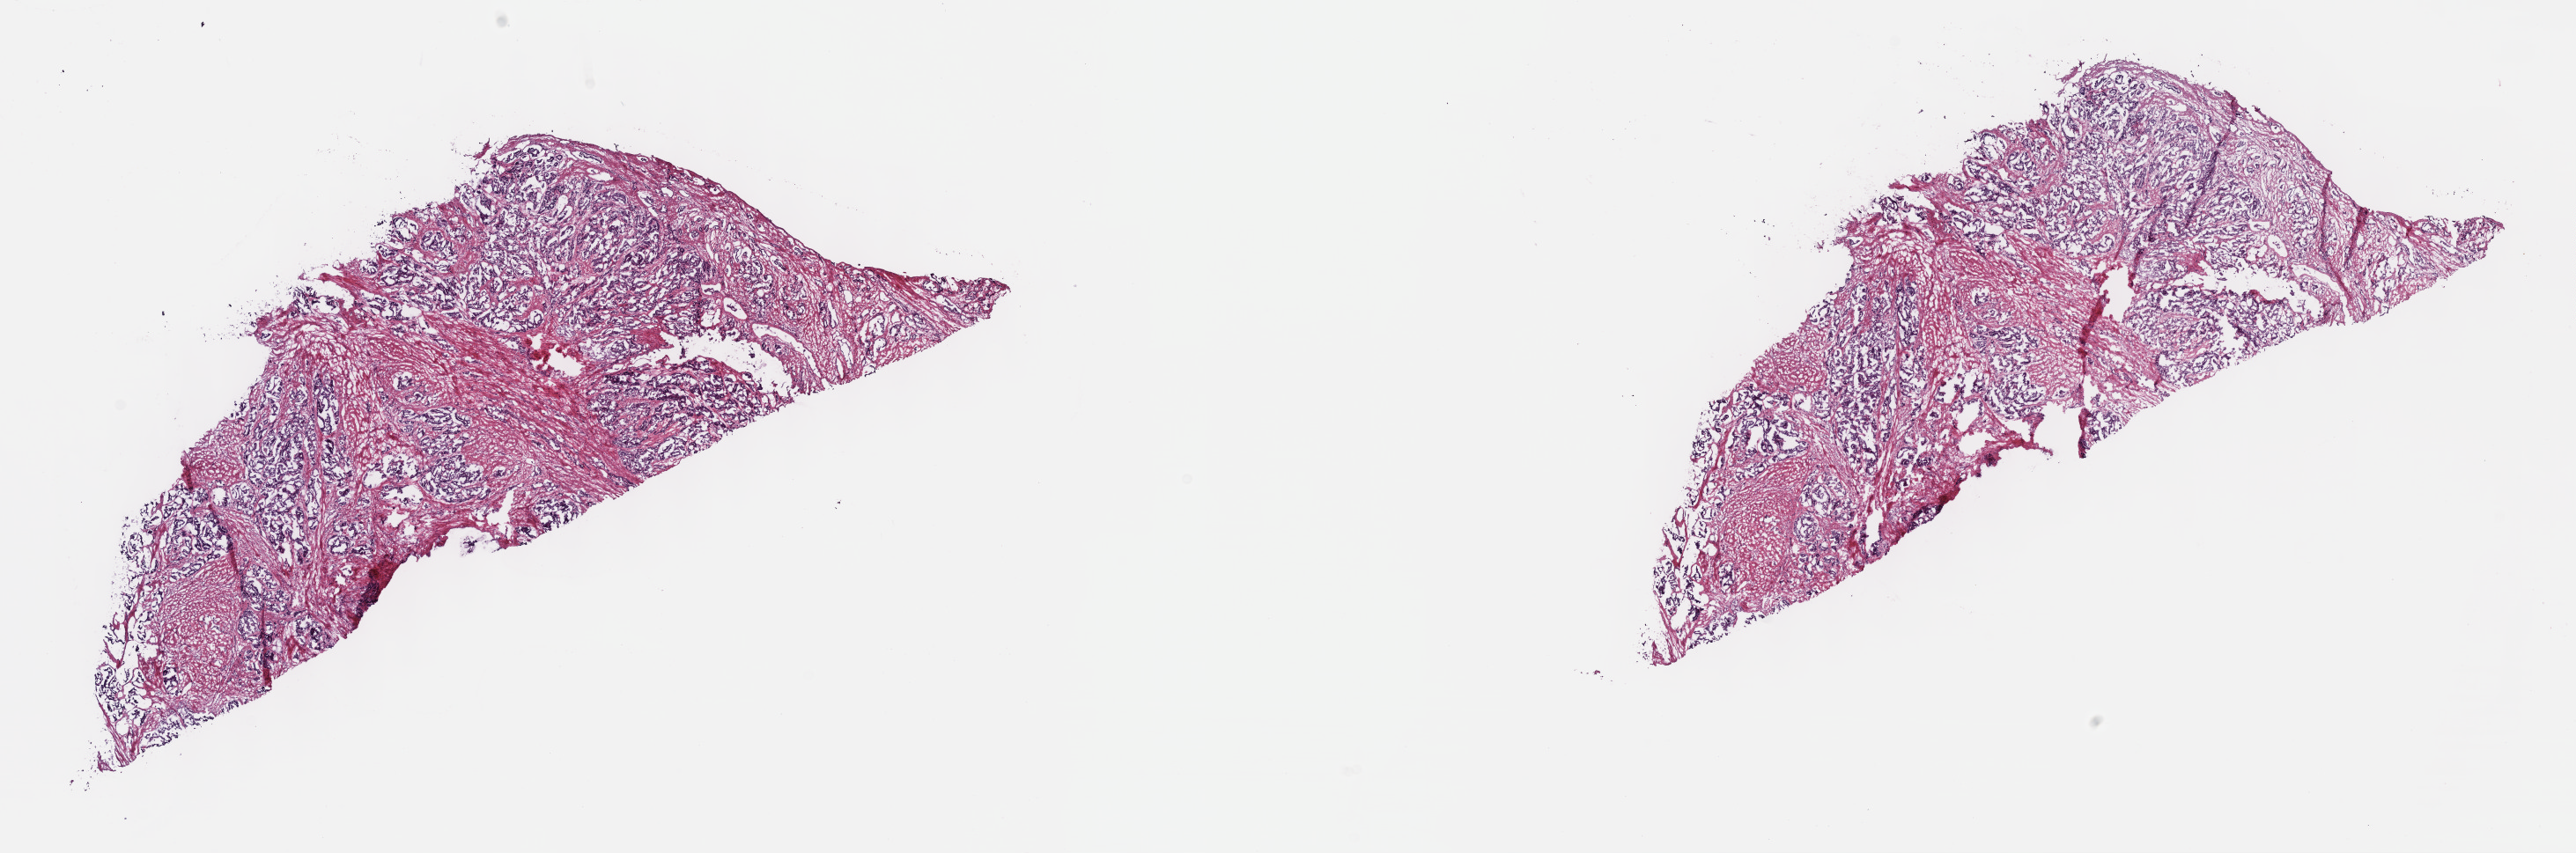
Whole-slide histology image, H&E-stained, low-resolution overview of the scanned area, about 23.7 x 7.8 mm (from a 40x scan). Frozen section from the top of the tissue portion. Primary tumour sample from the prostate. Male, age 58 years at initial diagnosis. Gleason score: 8 (4+4). Composition of this section per pathologist review: tumour cells 70%, tumour nuclei 70%, normal cells 0%, stromal cells 30%, necrosis 0%. Infiltration values recorded for this section: lymphocyte infiltration 60%, monocyte infiltration 10%, neutrophil infiltration 20%.
* diagnosis: Adenocarcinoma, NOS
* lymph nodes positive (case pathology): 15 of 37 examined